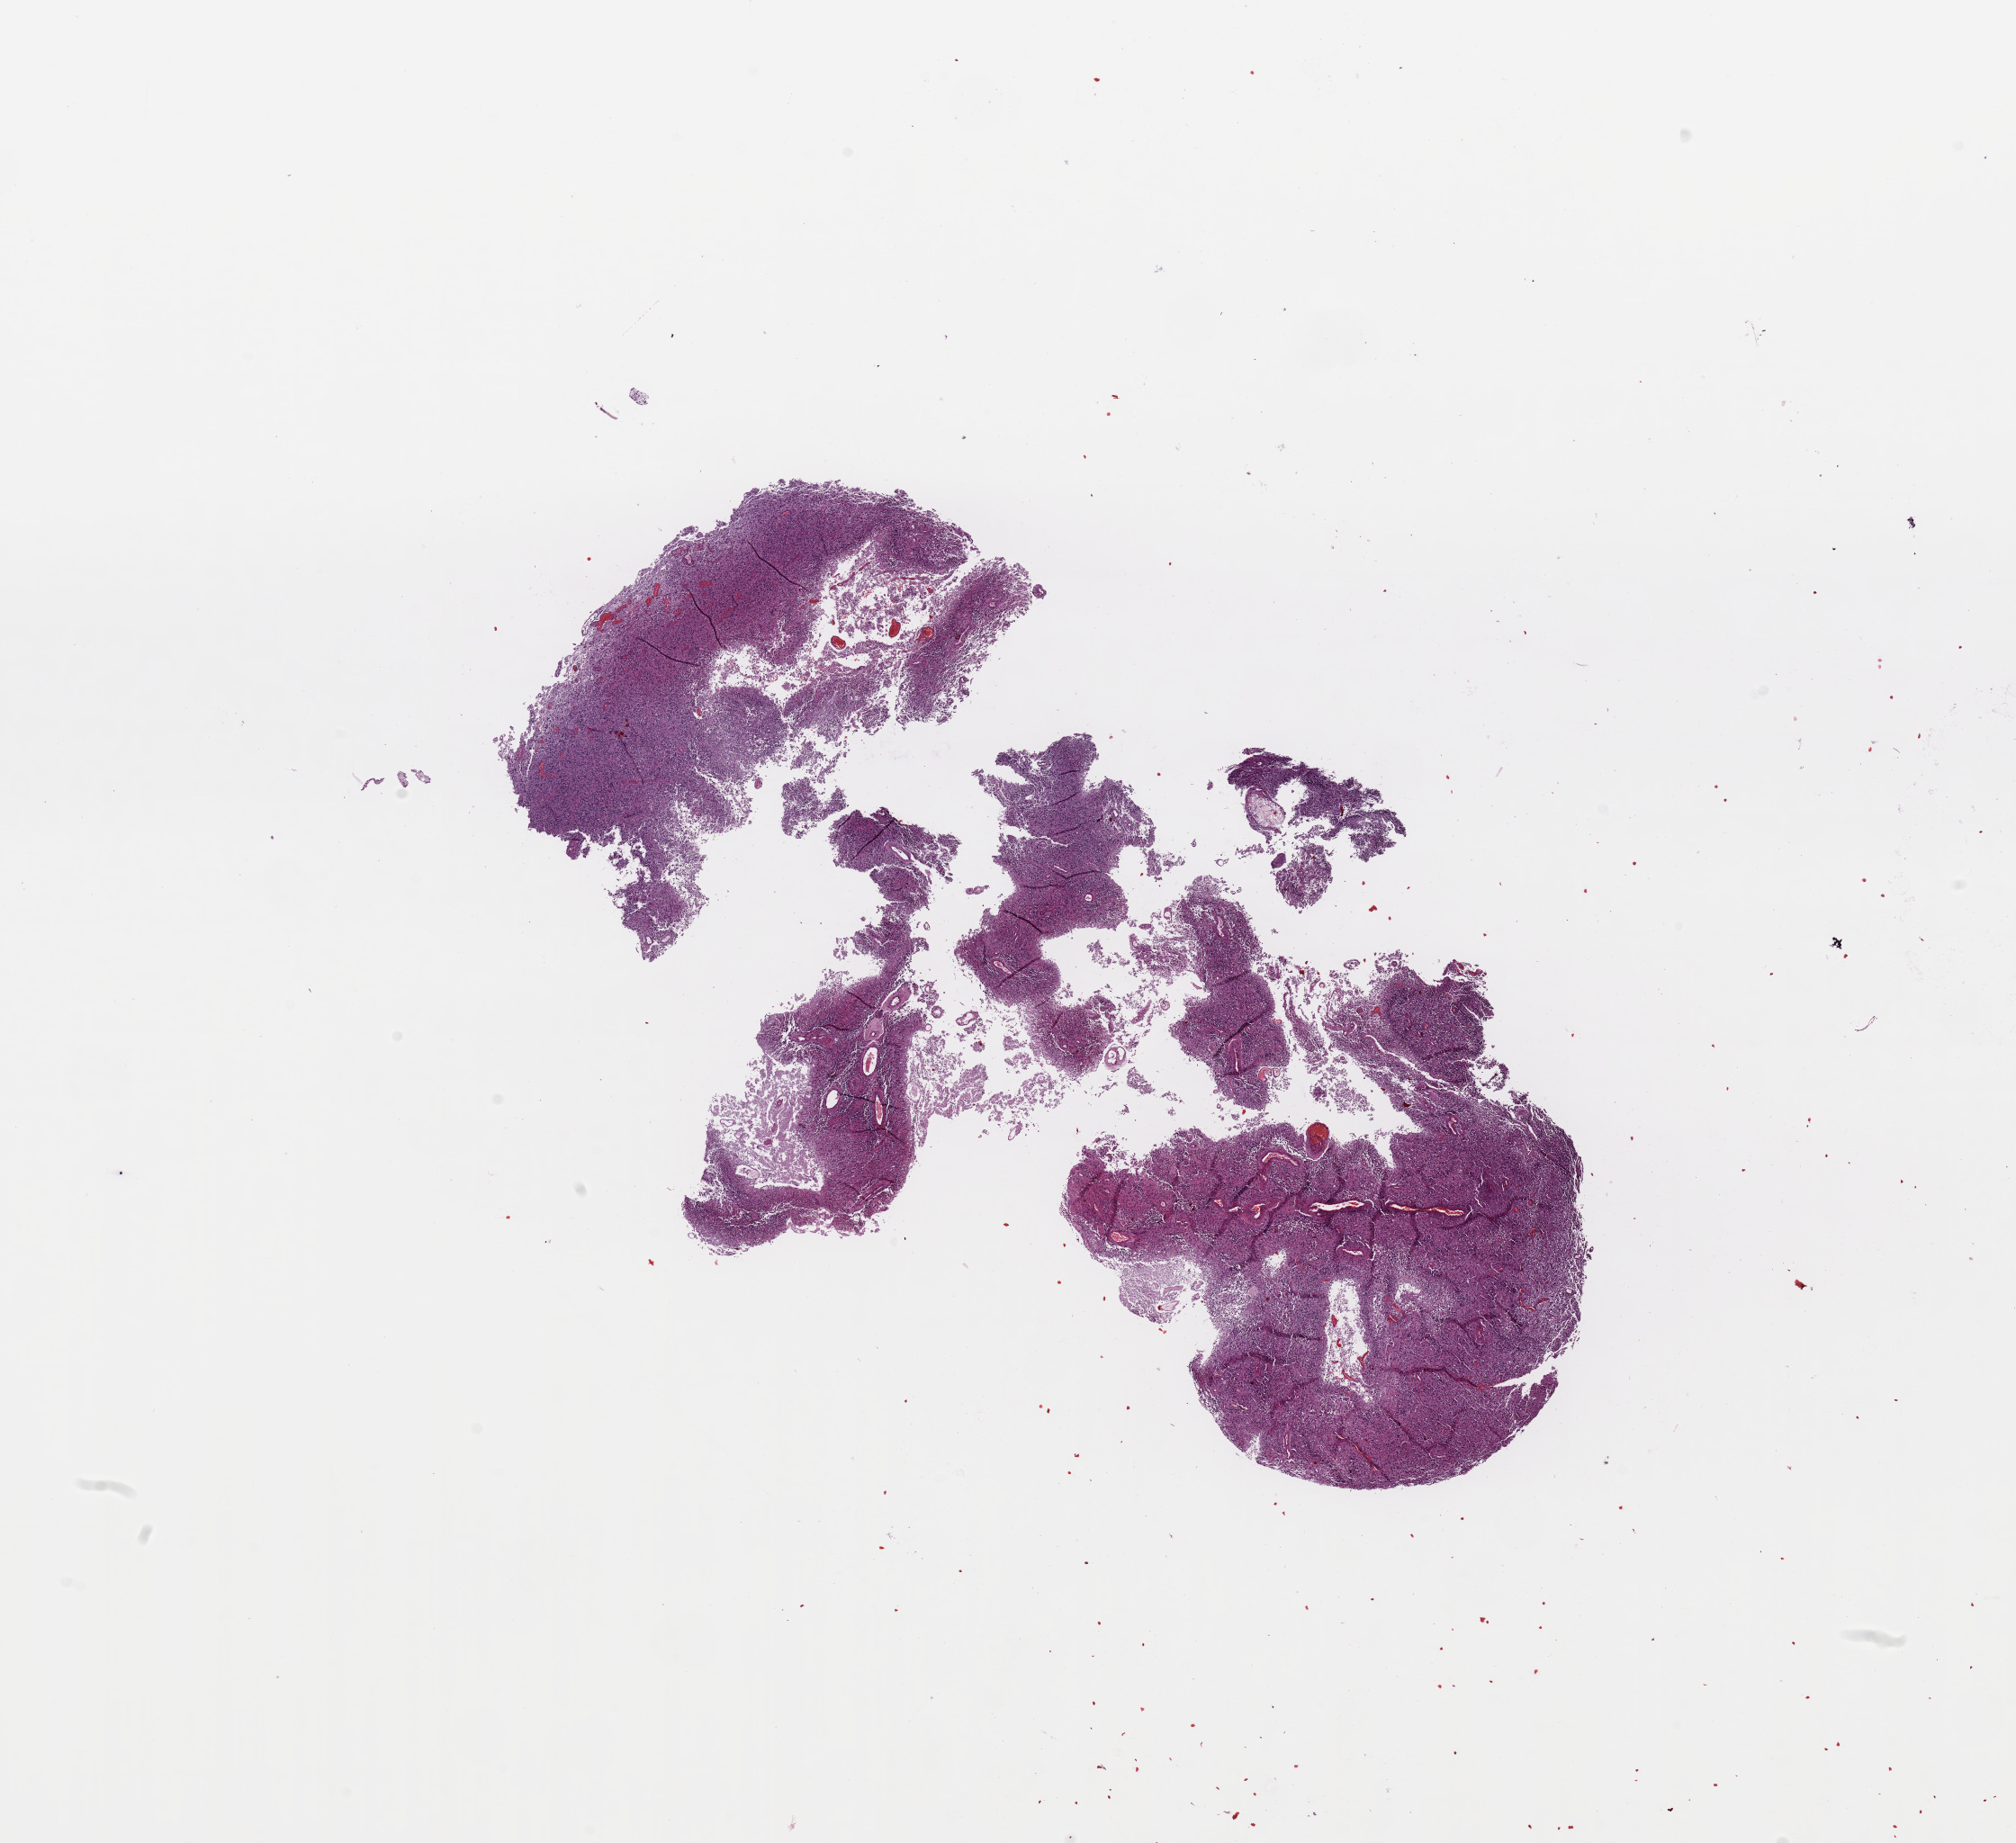
Whole-slide histology image, H&E-stained — shown as a low-resolution overview of the whole scanned area (about 17.7 x 16.2 mm). Tumour tissue sample, sampled site: brain. 69-year-old male patient. Composition of this section per pathologist review: tumour nuclei 80%, necrosis 5%.
Diagnosis: Glioblastoma.